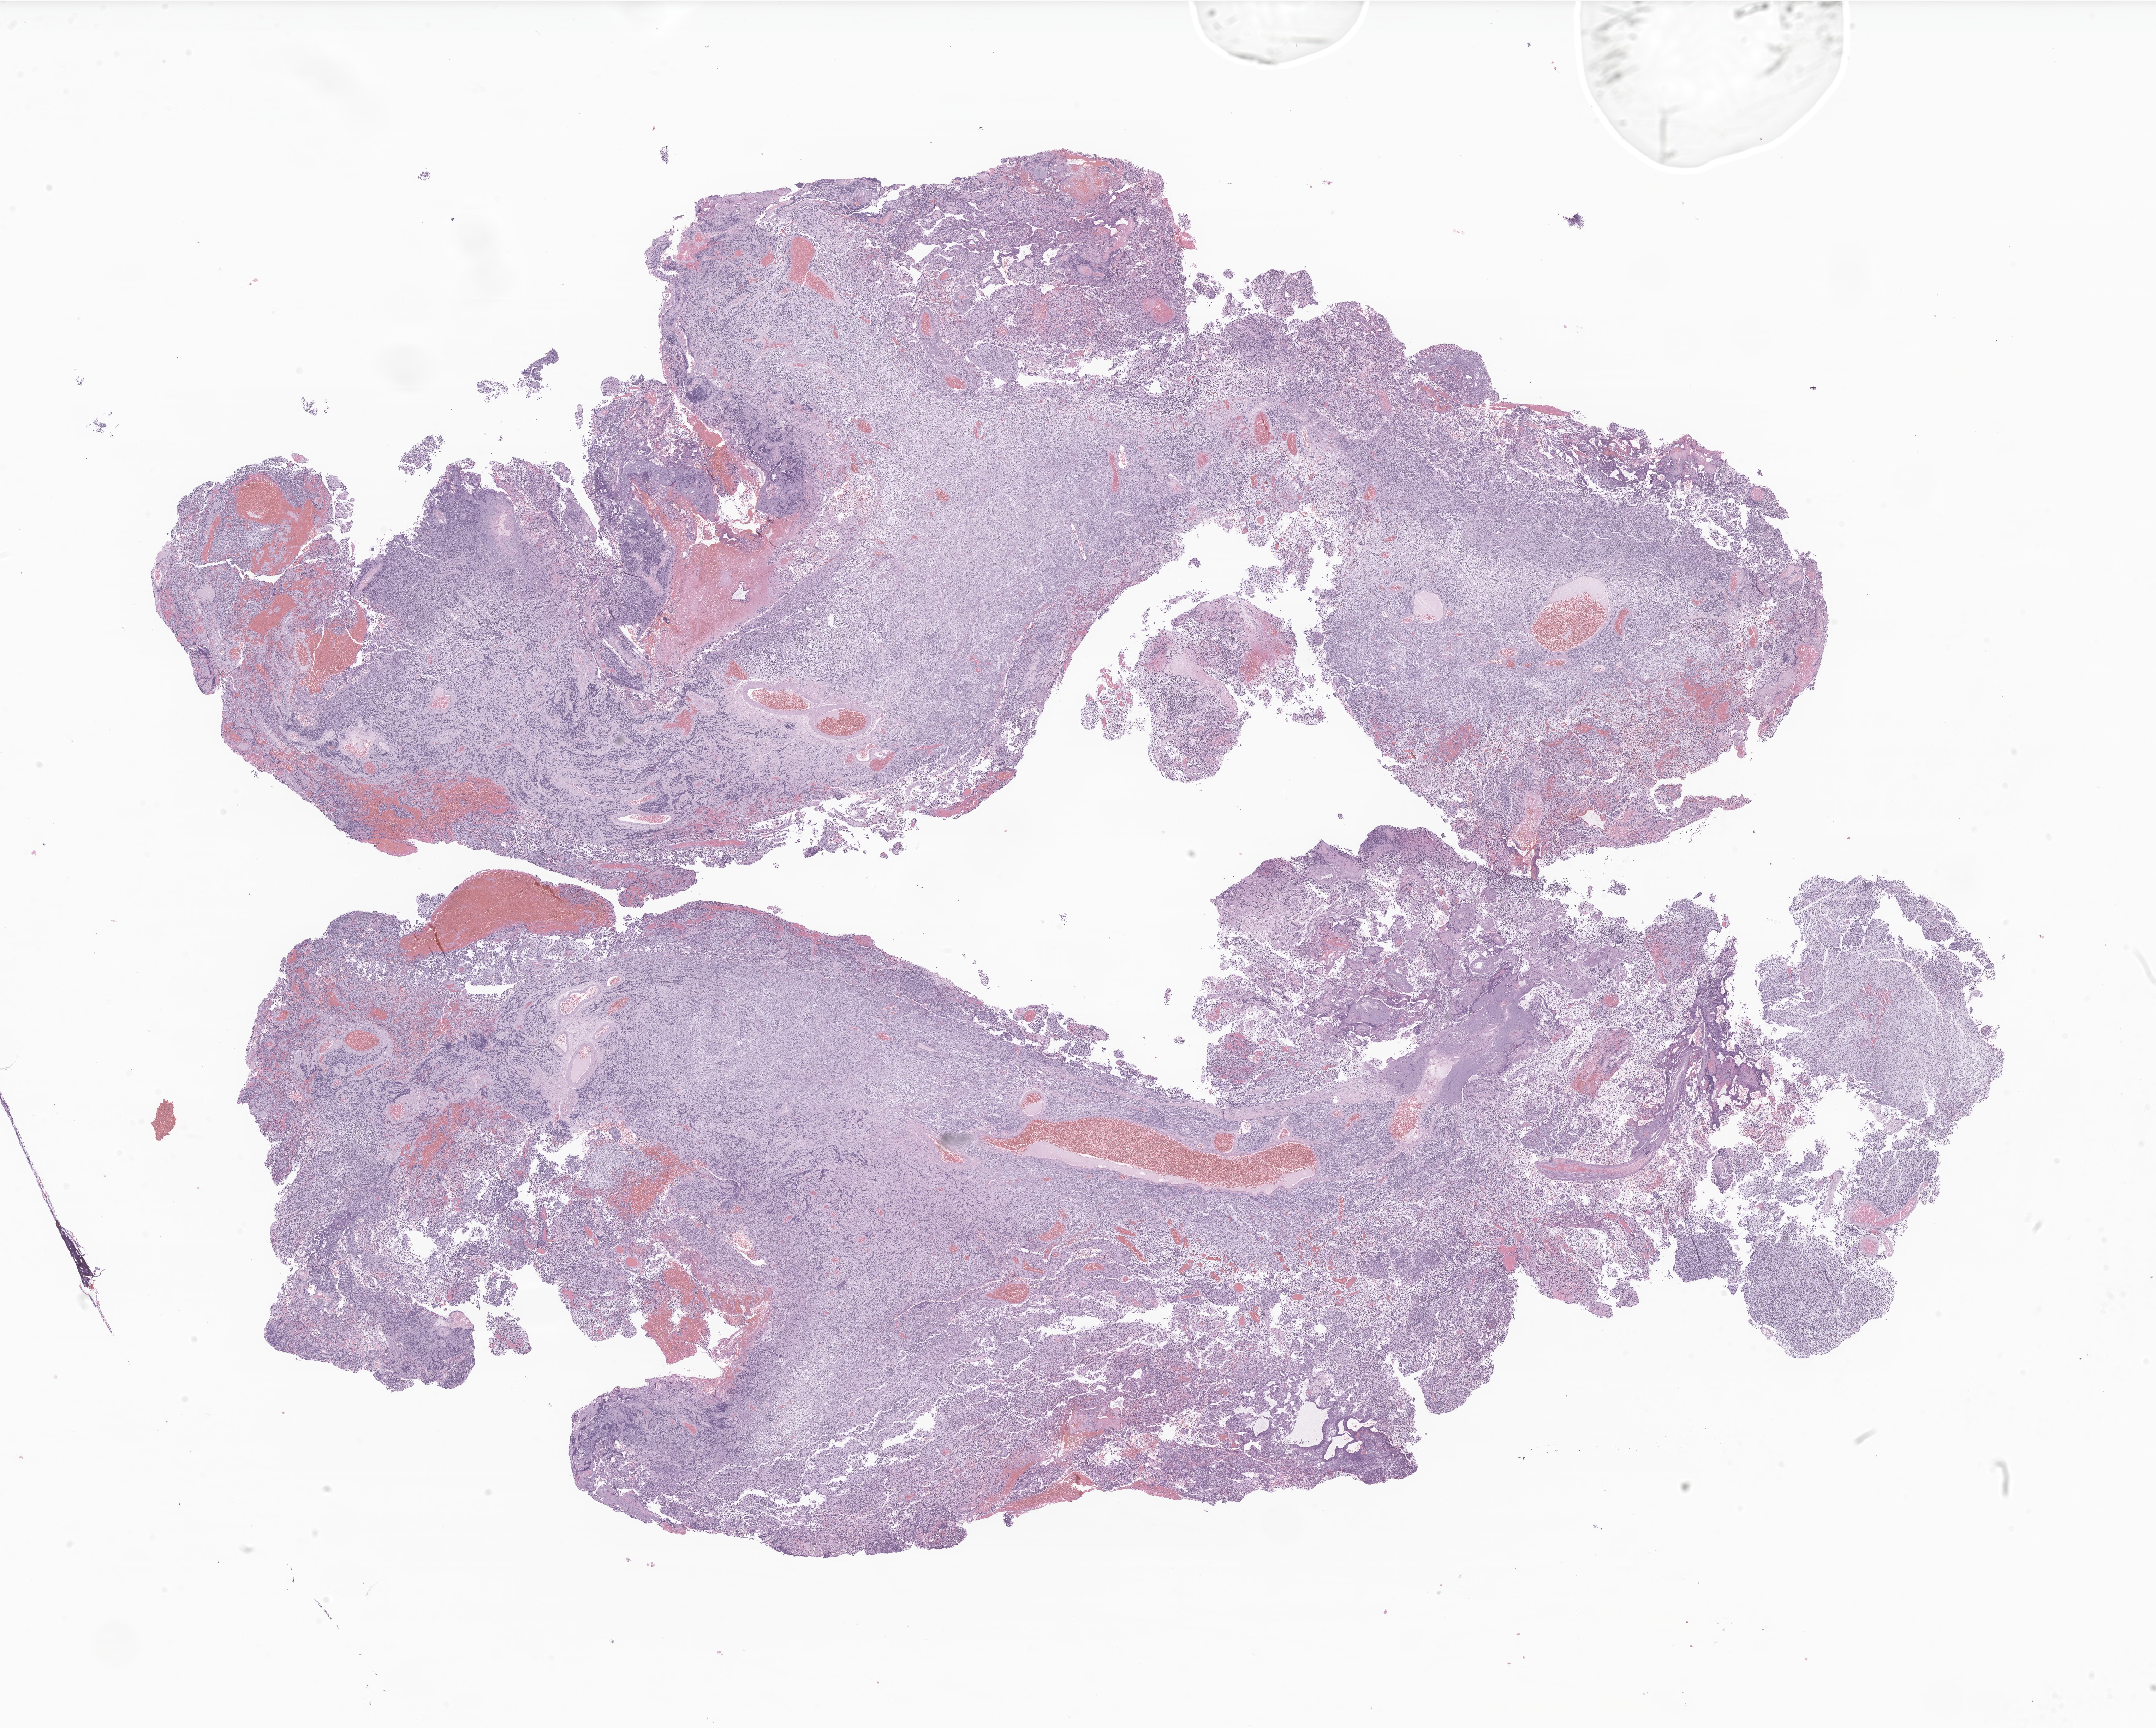
Whole-slide image, H&E stain of tumor tissue from the brain, shown as a low-resolution overview of the whole scanned area (about 25.7 x 20.6 mm), formalin-fixed, paraffin-embedded (FFPE) tissue. Patient: male, age 91 months (7 years 7 months).
- diagnosis: Medulloblastoma, NOS